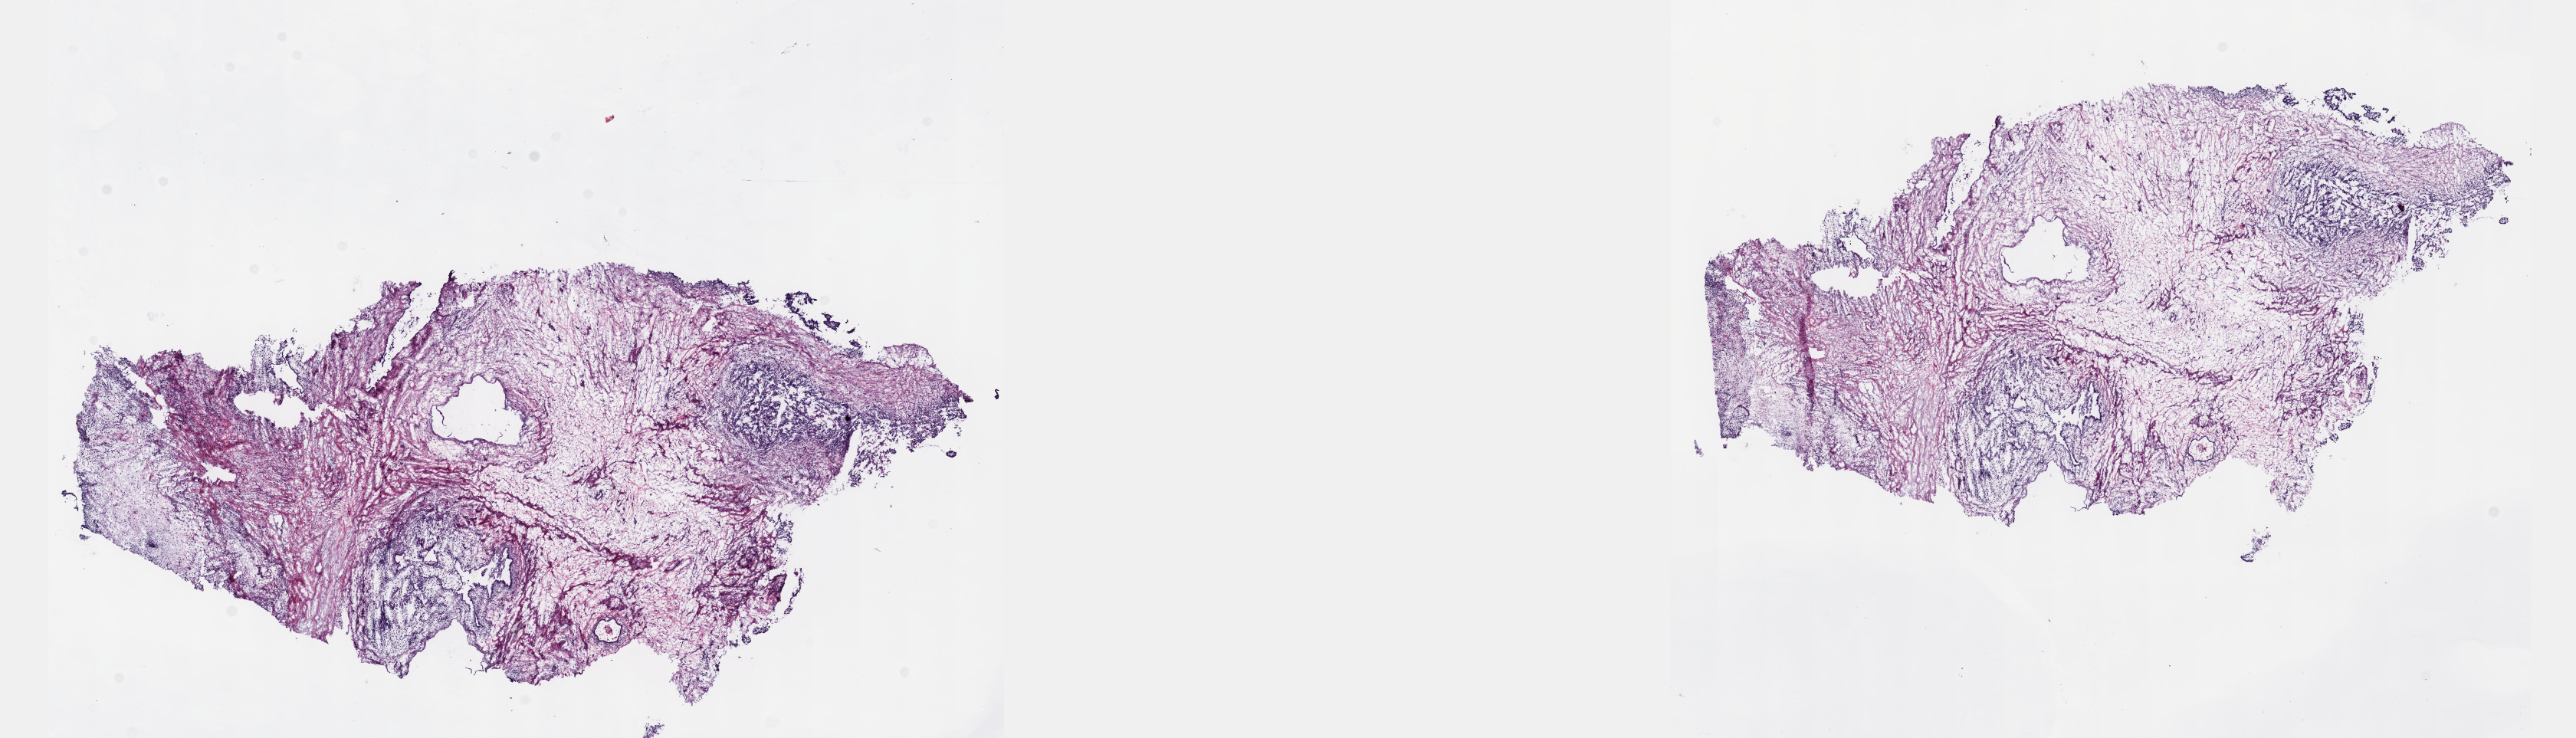
Whole-slide histology image, H&E-stained, shown as a low-resolution overview of the whole scanned area (about 27.2 x 7.8 mm), frozen section, sample: primary tumour, testis. Patient: male, age at initial diagnosis 33 years. Slide review estimates, as recorded: tumour cells 70%, tumour nuclei 70%, normal cells 0%, stromal cells 30%, necrosis 0%. Inflammatory infiltration, as recorded: lymphocyte infiltration 40%, monocyte infiltration 20%, neutrophil infiltration 20%.
• AJCC pathologic stage: IS
• histologic diagnosis: Mixed germ cell tumor
• laterality: right